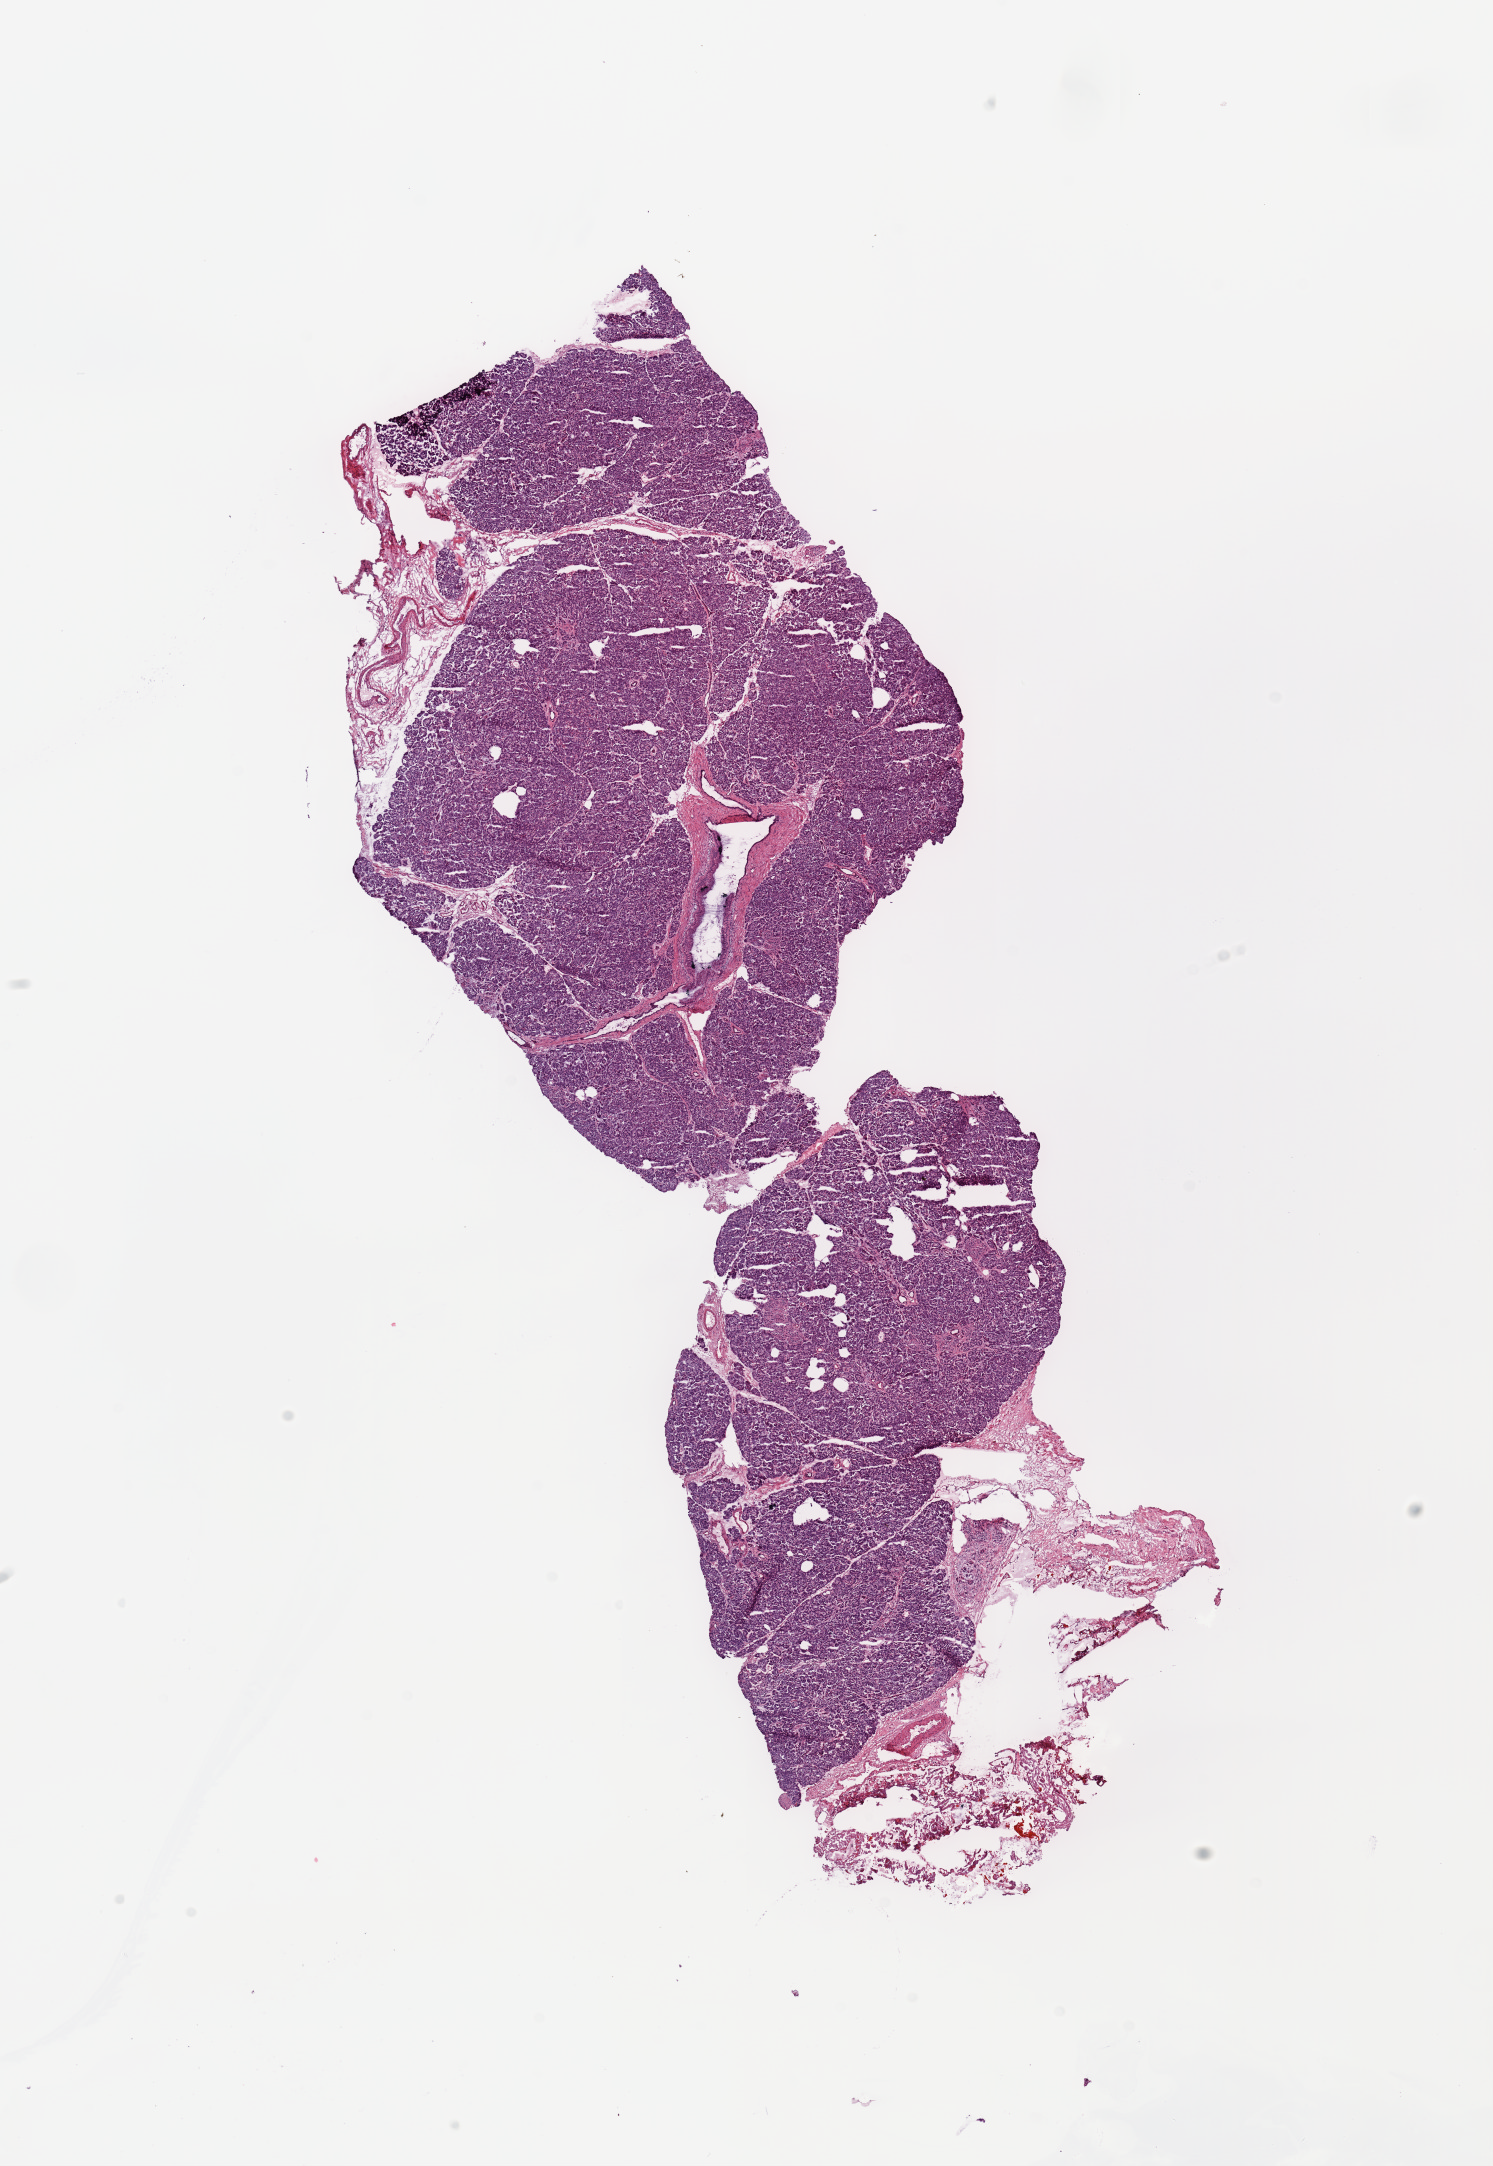
Hematoxylin and eosin (H&E) stained whole-slide image, a low-resolution overview of the entire scanned area, about 11.8 x 17.1 mm (acquisition: 20x scan), normal (non-tumour) tissue sample, sampled site: pancreas. Patient: male, age 69 years.
This section: normal (non-tumour) tissue from the same patient. Patient diagnosis: Infiltrating duct carcinoma, NOS.